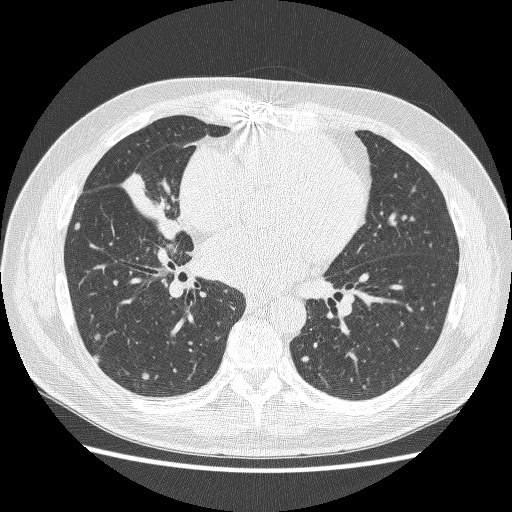
Low-dose screening chest CT, axial slice; first (baseline) screen; lung window (W 1500 / L -600 HU); 1.25 mm slice thickness; lung (sharp) reconstruction kernel (BONE); slice 125 of 251 in the series. Male, age 59 years at enrolment. Former smoker at enrolment.
• Expert-annotated lung lesion, bounding box (x1, y1, x2, y2) in pixels: (111, 162, 195, 248).
• No non-calcified nodule or mass ≥4 mm was recorded by the screening reader at this exam.
• Participant outcome: lung cancer diagnosed 24 days after this screen — adenocarcinoma, NOS, right middle lobe, poorly differentiated (G3), stage IV (AJCC 6th edition), 54 mm at pathology.